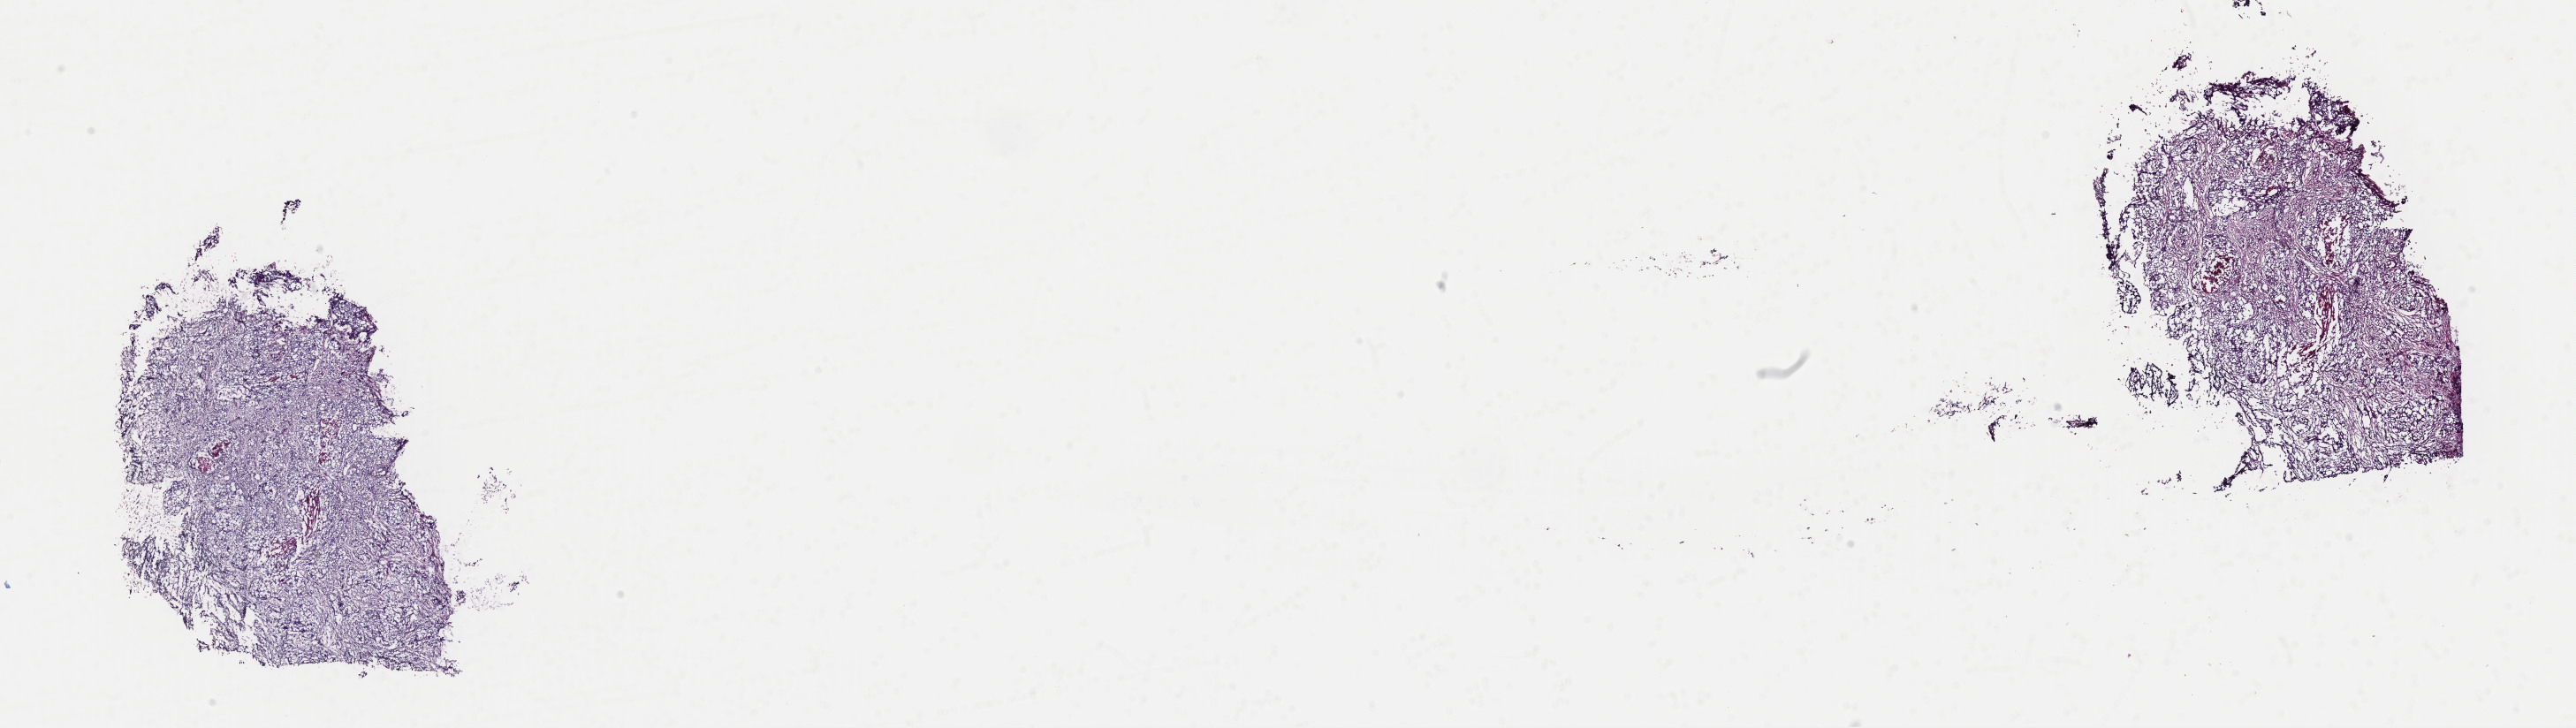
Digitized H&E tissue section (whole slide) — whole scanned area (about 23.0 x 6.5 mm, acquisition: 40x scan) shown as a low-resolution overview, frozen section from the top of the tissue portion, primary tumour sample from the lung. Patient: male, age at initial diagnosis 75 years. Composition of this section per pathologist review: tumour cells 50%, tumour nuclei 60%, normal cells 0%, stromal cells 40%, necrosis 10%. Infiltration values recorded for this section: lymphocyte infiltration 12%, monocyte infiltration 2%, neutrophil infiltration 2%.
AJCC pathologic stage: IIIA (6th edition). Histologic diagnosis: Squamous cell carcinoma, NOS (lower lobe, lung). TNM: T3 N1 M0.